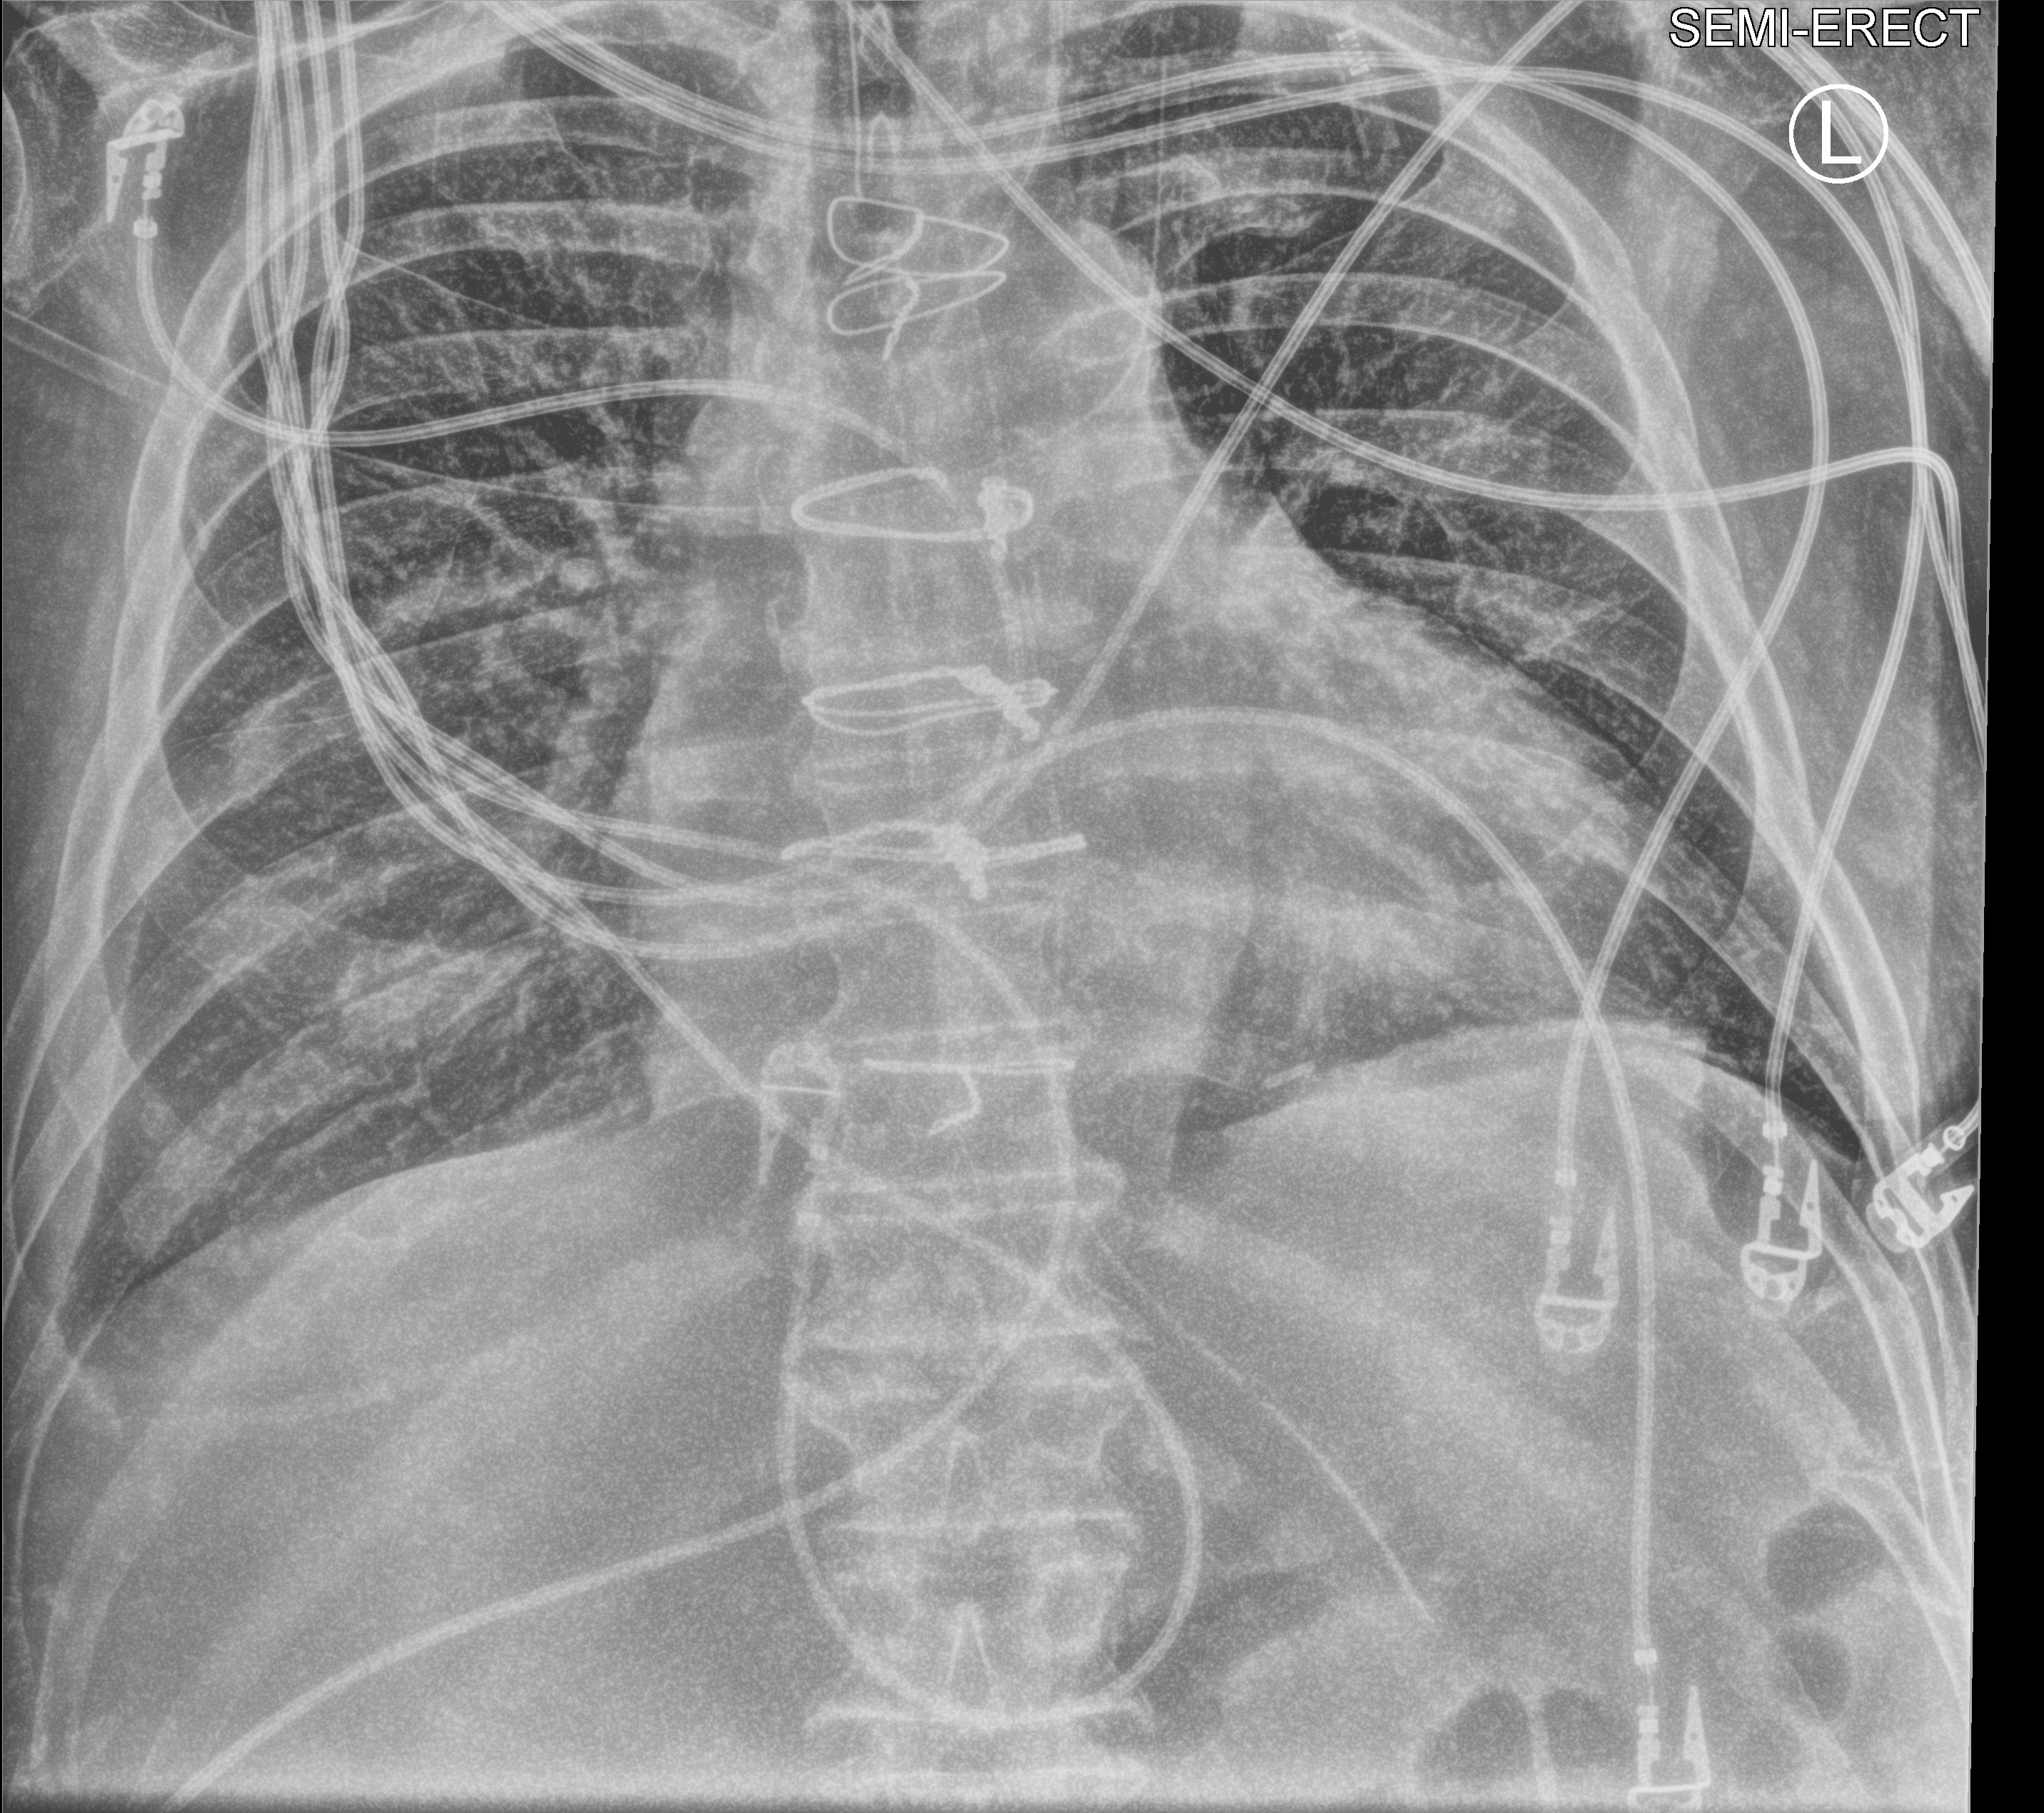
Bedside chest radiograph (computed radiography); anteroposterior (AP) projection. Patient hospitalised with COVID-19; male, aged 60–74 years.
Admission-level facts for this patient (not findings on this image; timing relative to this image not recorded):
- admitted to intensive care during this hospital stay: yes
- hypertension (admission record): yes